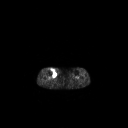
FDG PET of an extremity soft-tissue mass (from a PET/CT study), one axial slice; slice 143 of 267 in the series (ordered by position); 3.27 mm slice thickness; 128 × 128 image matrix, field of view 700 × 700 mm. Female patient, age 65 years. Case-level facts recorded for this patient, not image findings: histological type: undifferentiated – high grade; grade: high; site of the primary tumour: right thigh.
Outlined on this slice (expert contour drawn on MRI and transferred to this co-registered scan by the dataset authors):
- gross tumour volume (mass): bounding box <50,68,57,77> (left, top, right, bottom; pixels)